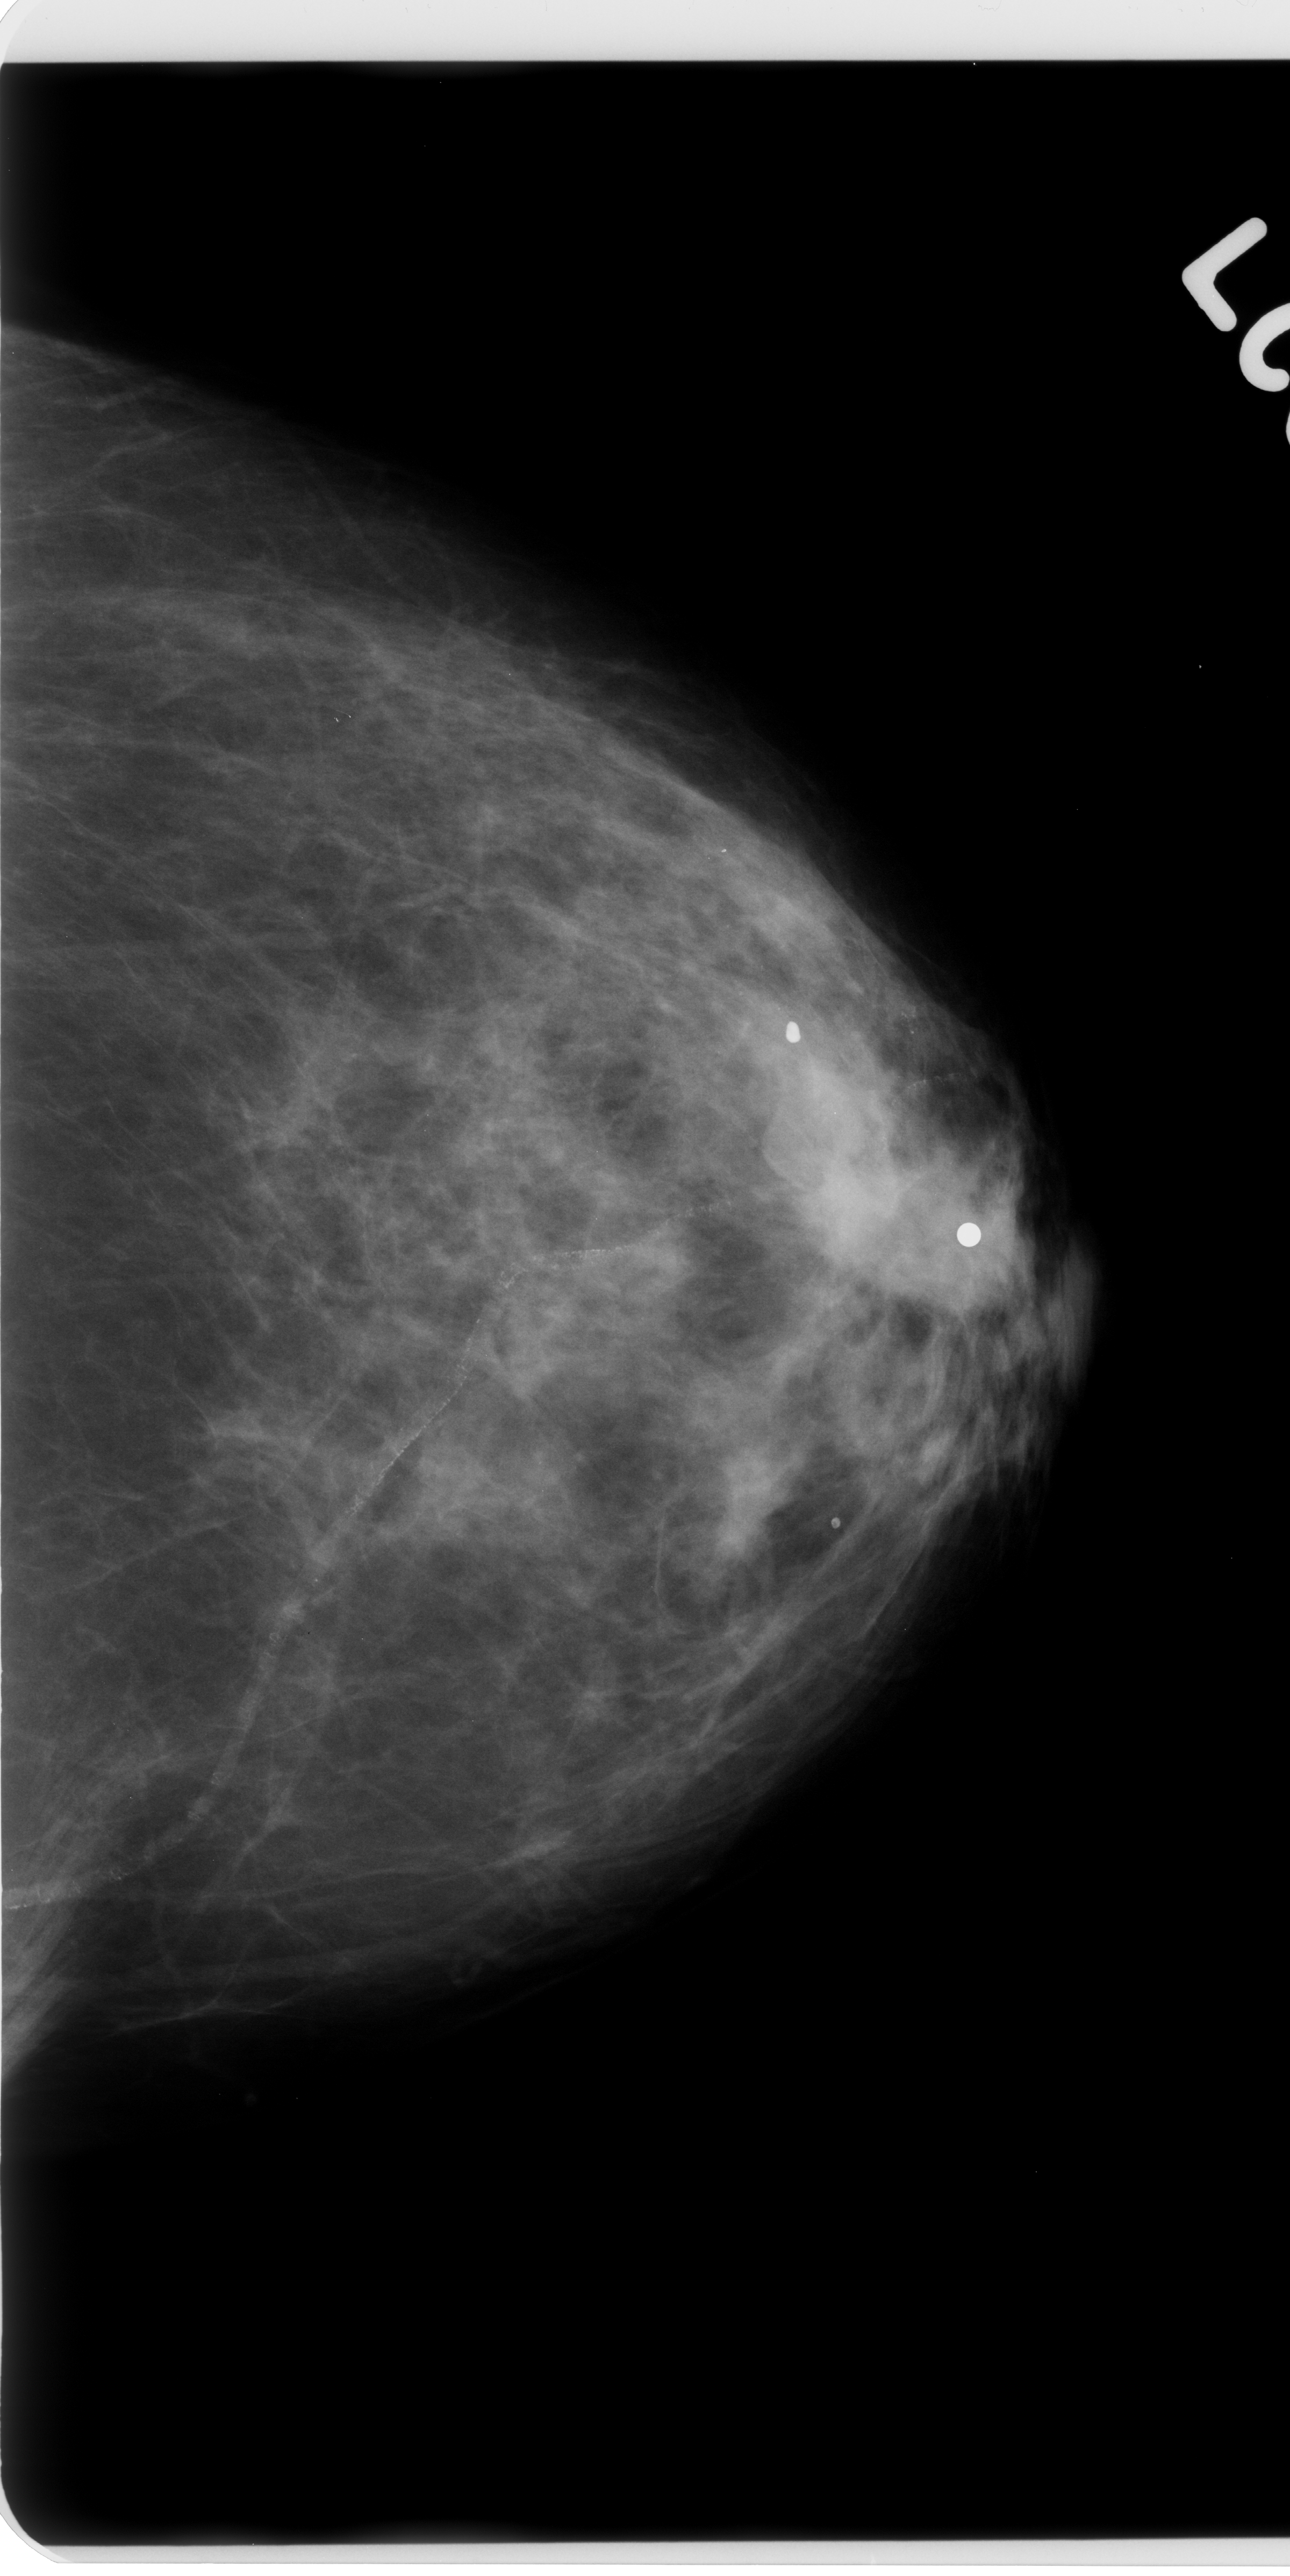
Mammogram (digitized film); left breast; craniocaudal (CC) view; breast composition: scattered fibroglandular densities (BI-RADS density category 2 of 4); 1290 × 2576 image matrix.
Expert-marked regions of interest on this film, with their recorded descriptors:
- mass, shape irregular, margins spiculated; BI-RADS assessment category 4; pathology (as recorded): malignant: bounding box [x1, y1, x2, y2] px = [800, 1134, 1031, 1317]